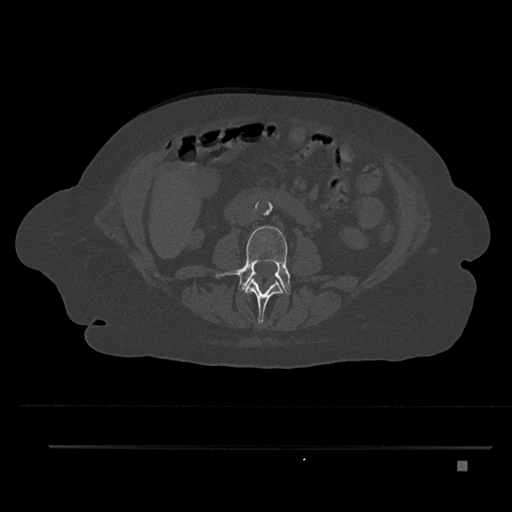
CT including the spine, one axial slice; slice 145 of 797 in the series (ordered by position); reconstruction kernel Br40s/3; bone window (W 1800 / L 400 HU); 0.5 mm slice thickness; 512 × 512 image matrix. Female patient, age 76 years. From the clinical record (not read from this slice): primary cancer: lung.
Outlined on this slice (semi-automatic segmentation, software-assisted and operator-edited):
- L2 vertebra: bounding box [x1, y1, x2, y2] px = [245, 278, 283, 324]
- L3 vertebra: [216, 226, 291, 295]